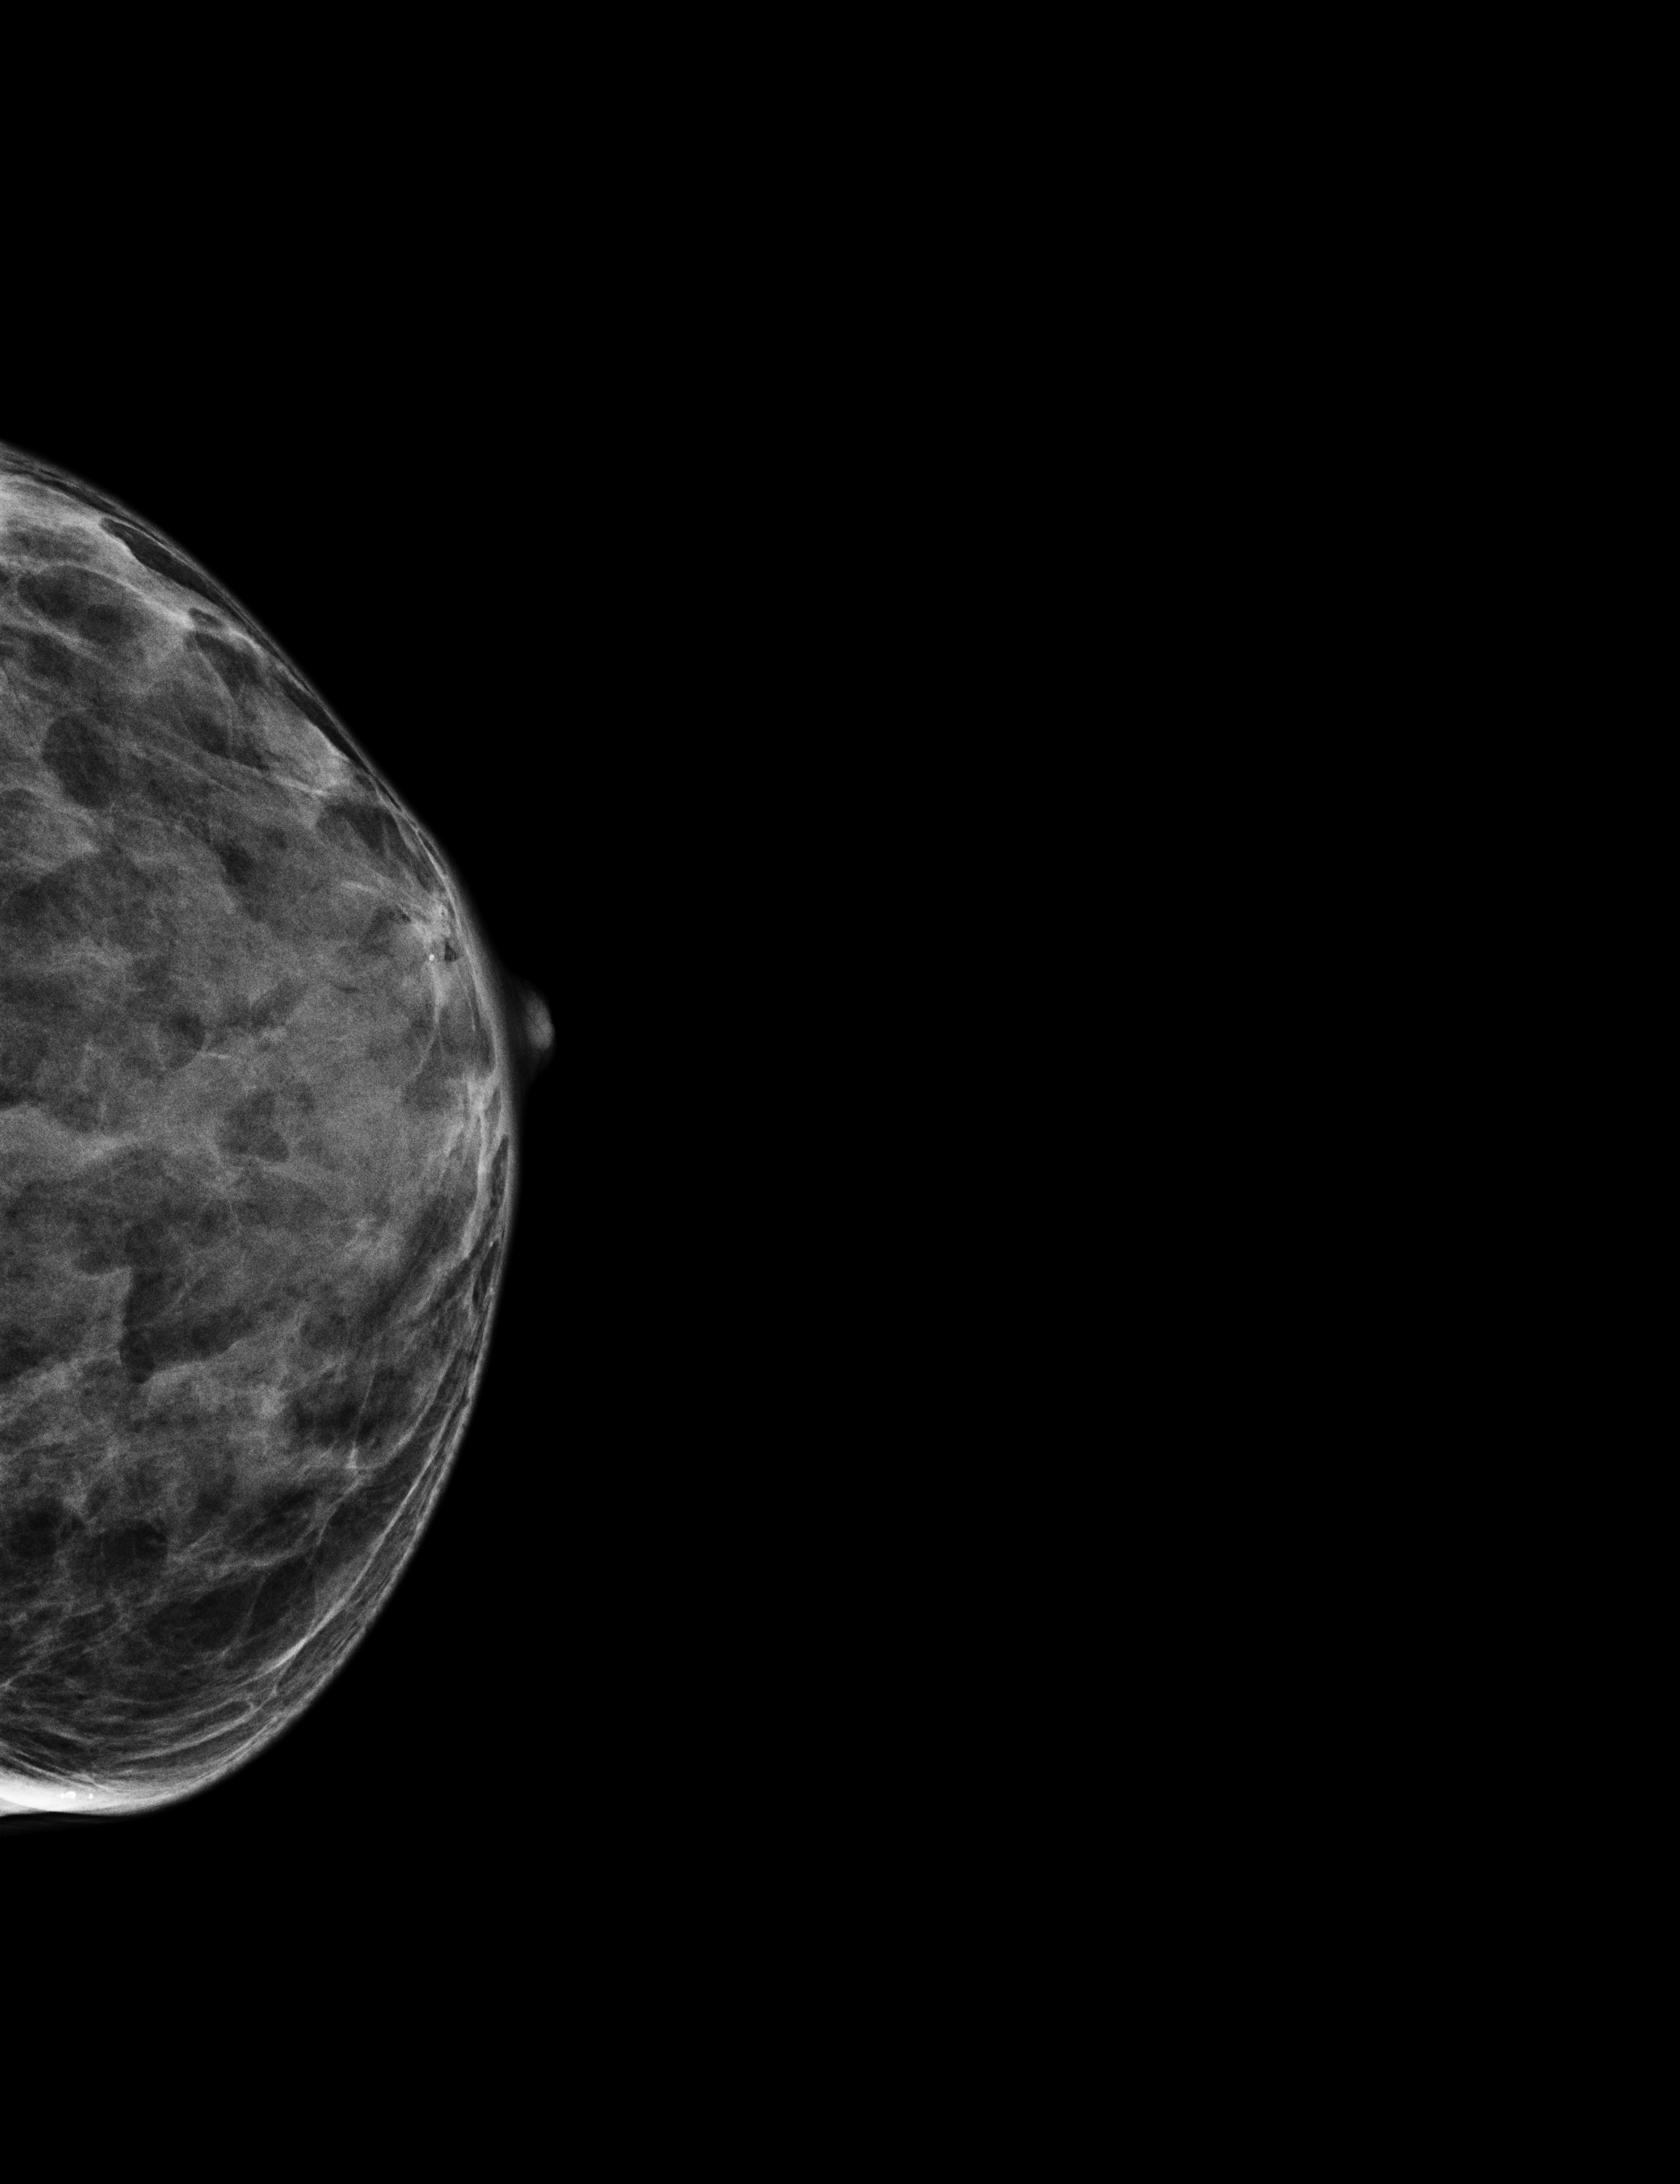
Annual screening mammography examination; compressed breast thickness 19 mm. Patient: female, 69 years.
Image type: full-field digital mammogram. Breast: left. Projection: cranio-caudal projection.